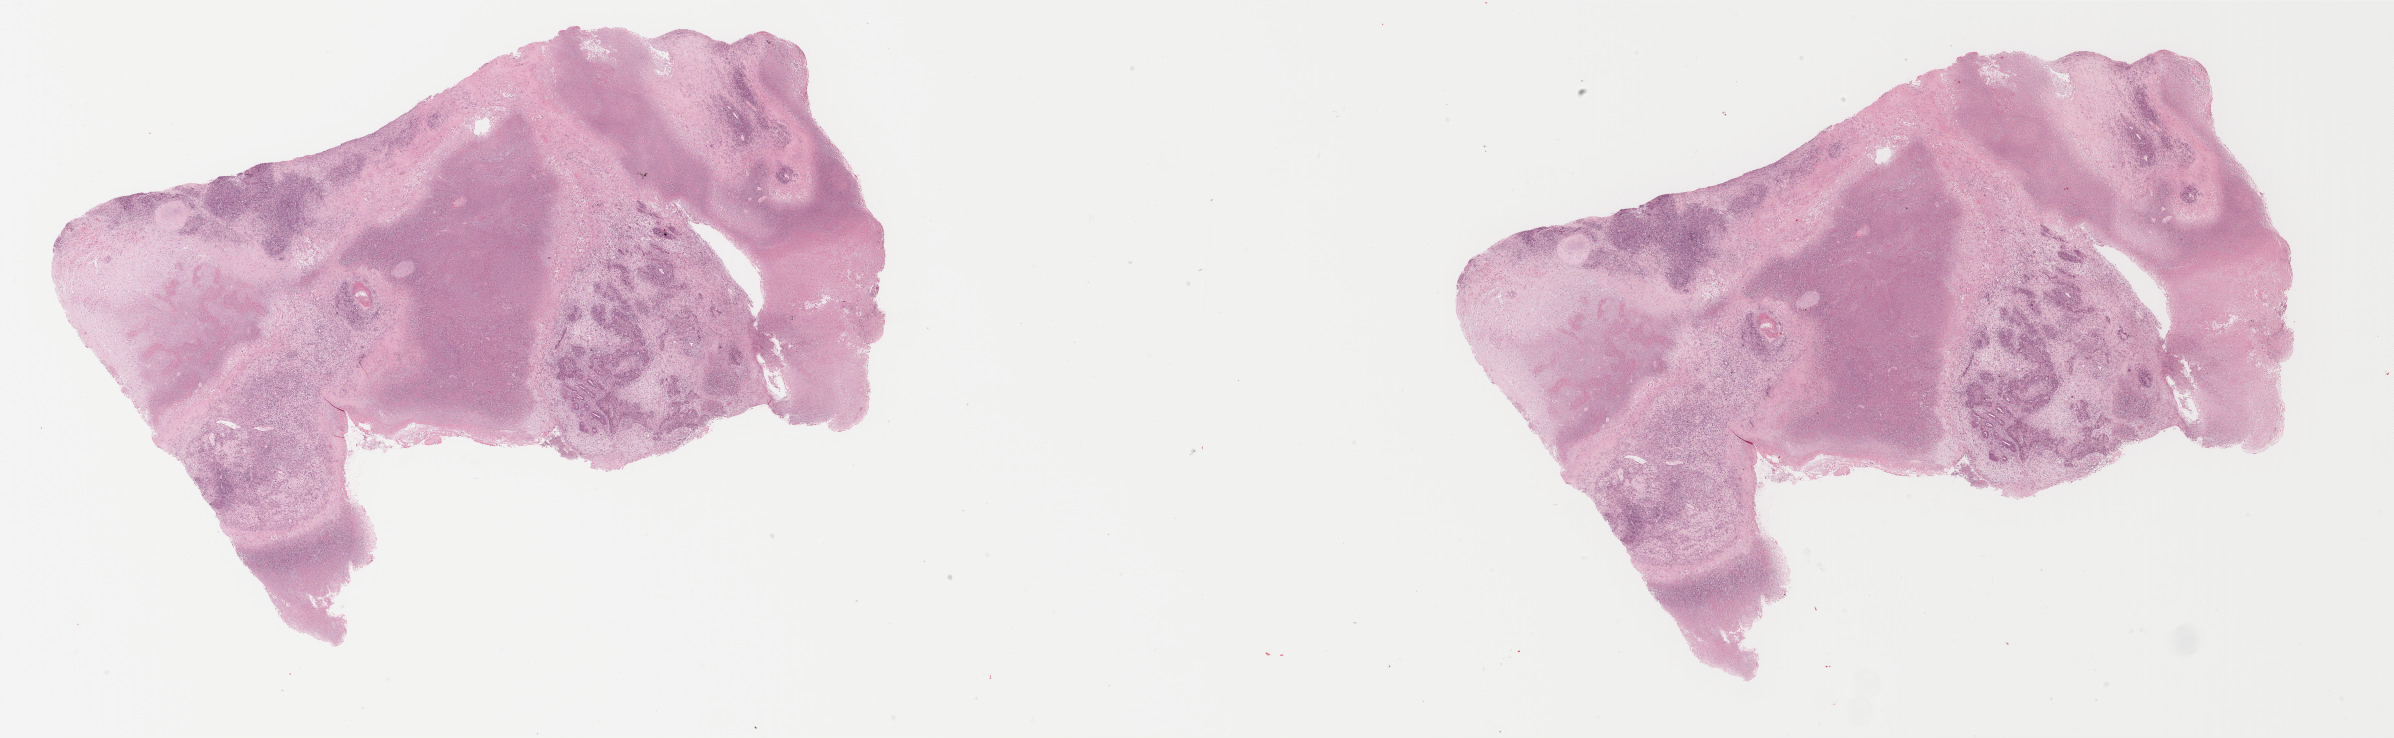
Digitized Hematoxylin and eosin (H&E) stained tissue section (whole slide) — shown as a low-resolution overview of the whole scanned area (about 38.0 x 11.7 mm, acquisition: 40x scan), FFPE section, sample: primary tumour, uterus. Patient: female, age at initial diagnosis 69 years.
Histologic diagnosis: Mullerian mixed tumor.